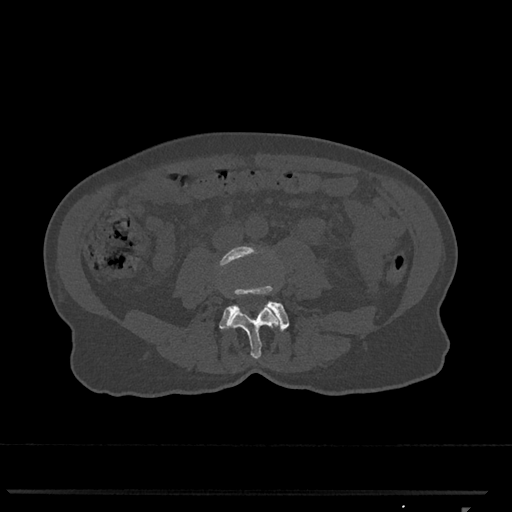
CT including the spine, one axial slice. Position 242 of 793 along the scan axis. 120 kVp. Bone window (W 1800 / L 400 HU). 0.5 mm slice thickness. 512 × 512 image matrix, field of view 380 × 380 mm. Patient: female, 62 years. Case-level facts recorded for this patient, not image findings: primary cancer: renal.
Outlined on this slice (semi-automatic segmentation, software-assisted and operator-edited):
- L3 vertebra: box from (x=219, y=246) to (x=281, y=359) px
- L4 vertebra: (x=219, y=286)–(x=289, y=332)